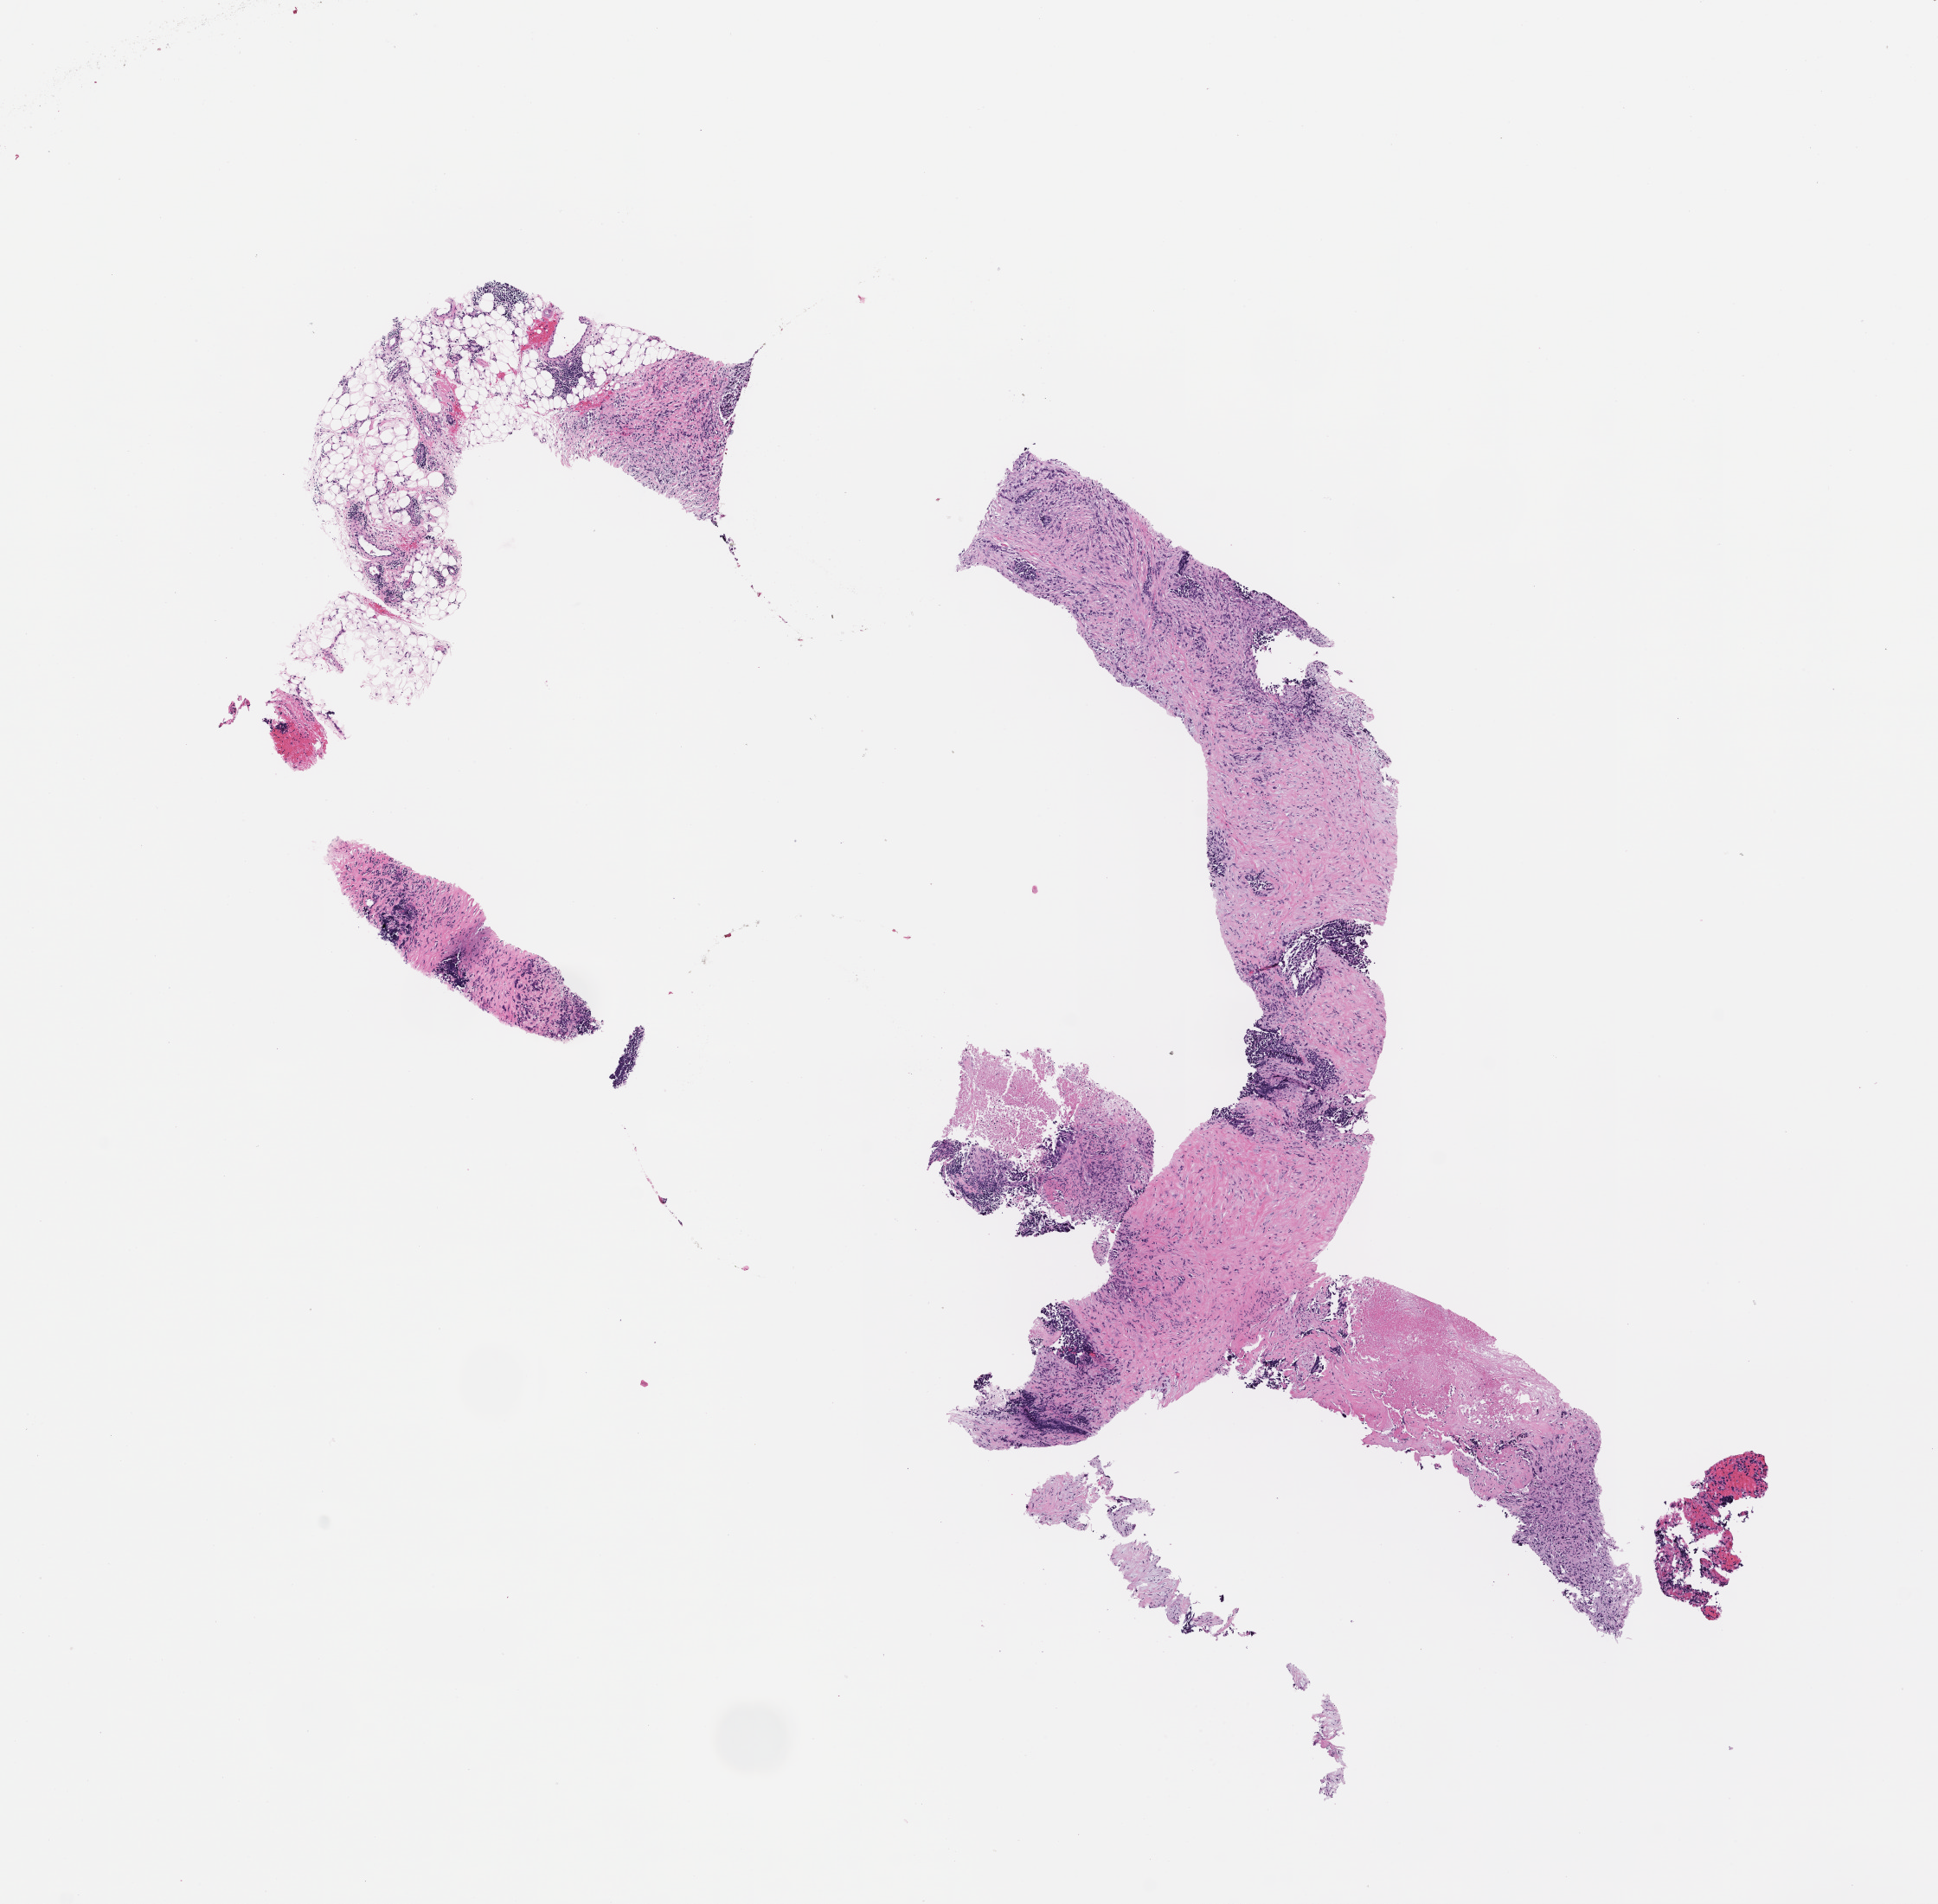
Whole-slide image, H&E stain — low-resolution overview of the scanned area, about 9.0 x 8.9 mm, formalin-fixed paraffin-embedded section, archival tissue. Female patient.
This section: metastasis (sampled organ not recorded). Primary diagnosis of the patient: Small Cell Lung Carcinoma.